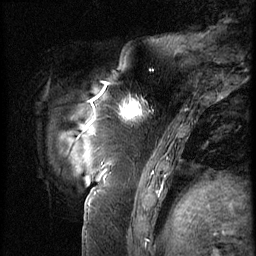
Breast MRI (dynamic contrast-enhanced), one sagittal slice. 3 images stored at this slice position (order not interpretable as contrast timing). 1.5 T. TE 4.2 ms, TR 9 ms. 2.5 mm slice thickness. 256 × 256 image matrix, field of view 180 × 180 mm. Patient: female, 57 years. From the clinical record (not read from this slice): setting: breast cancer imaged before/during neoadjuvant chemotherapy; receptor status: triple-negative.
Outlined on this slice (semi-automatically segmented with operator editing):
- analysis volume of interest (the breast-tissue region the enhancement analysis was run in; not a lesion): bounding box (x1, y1, x2, y2) in pixels: (105, 84, 158, 135)
- tumour enhancement mask (voxels above the 140 % enhancement threshold inside the analysis volume of interest): (105, 84, 144, 119)